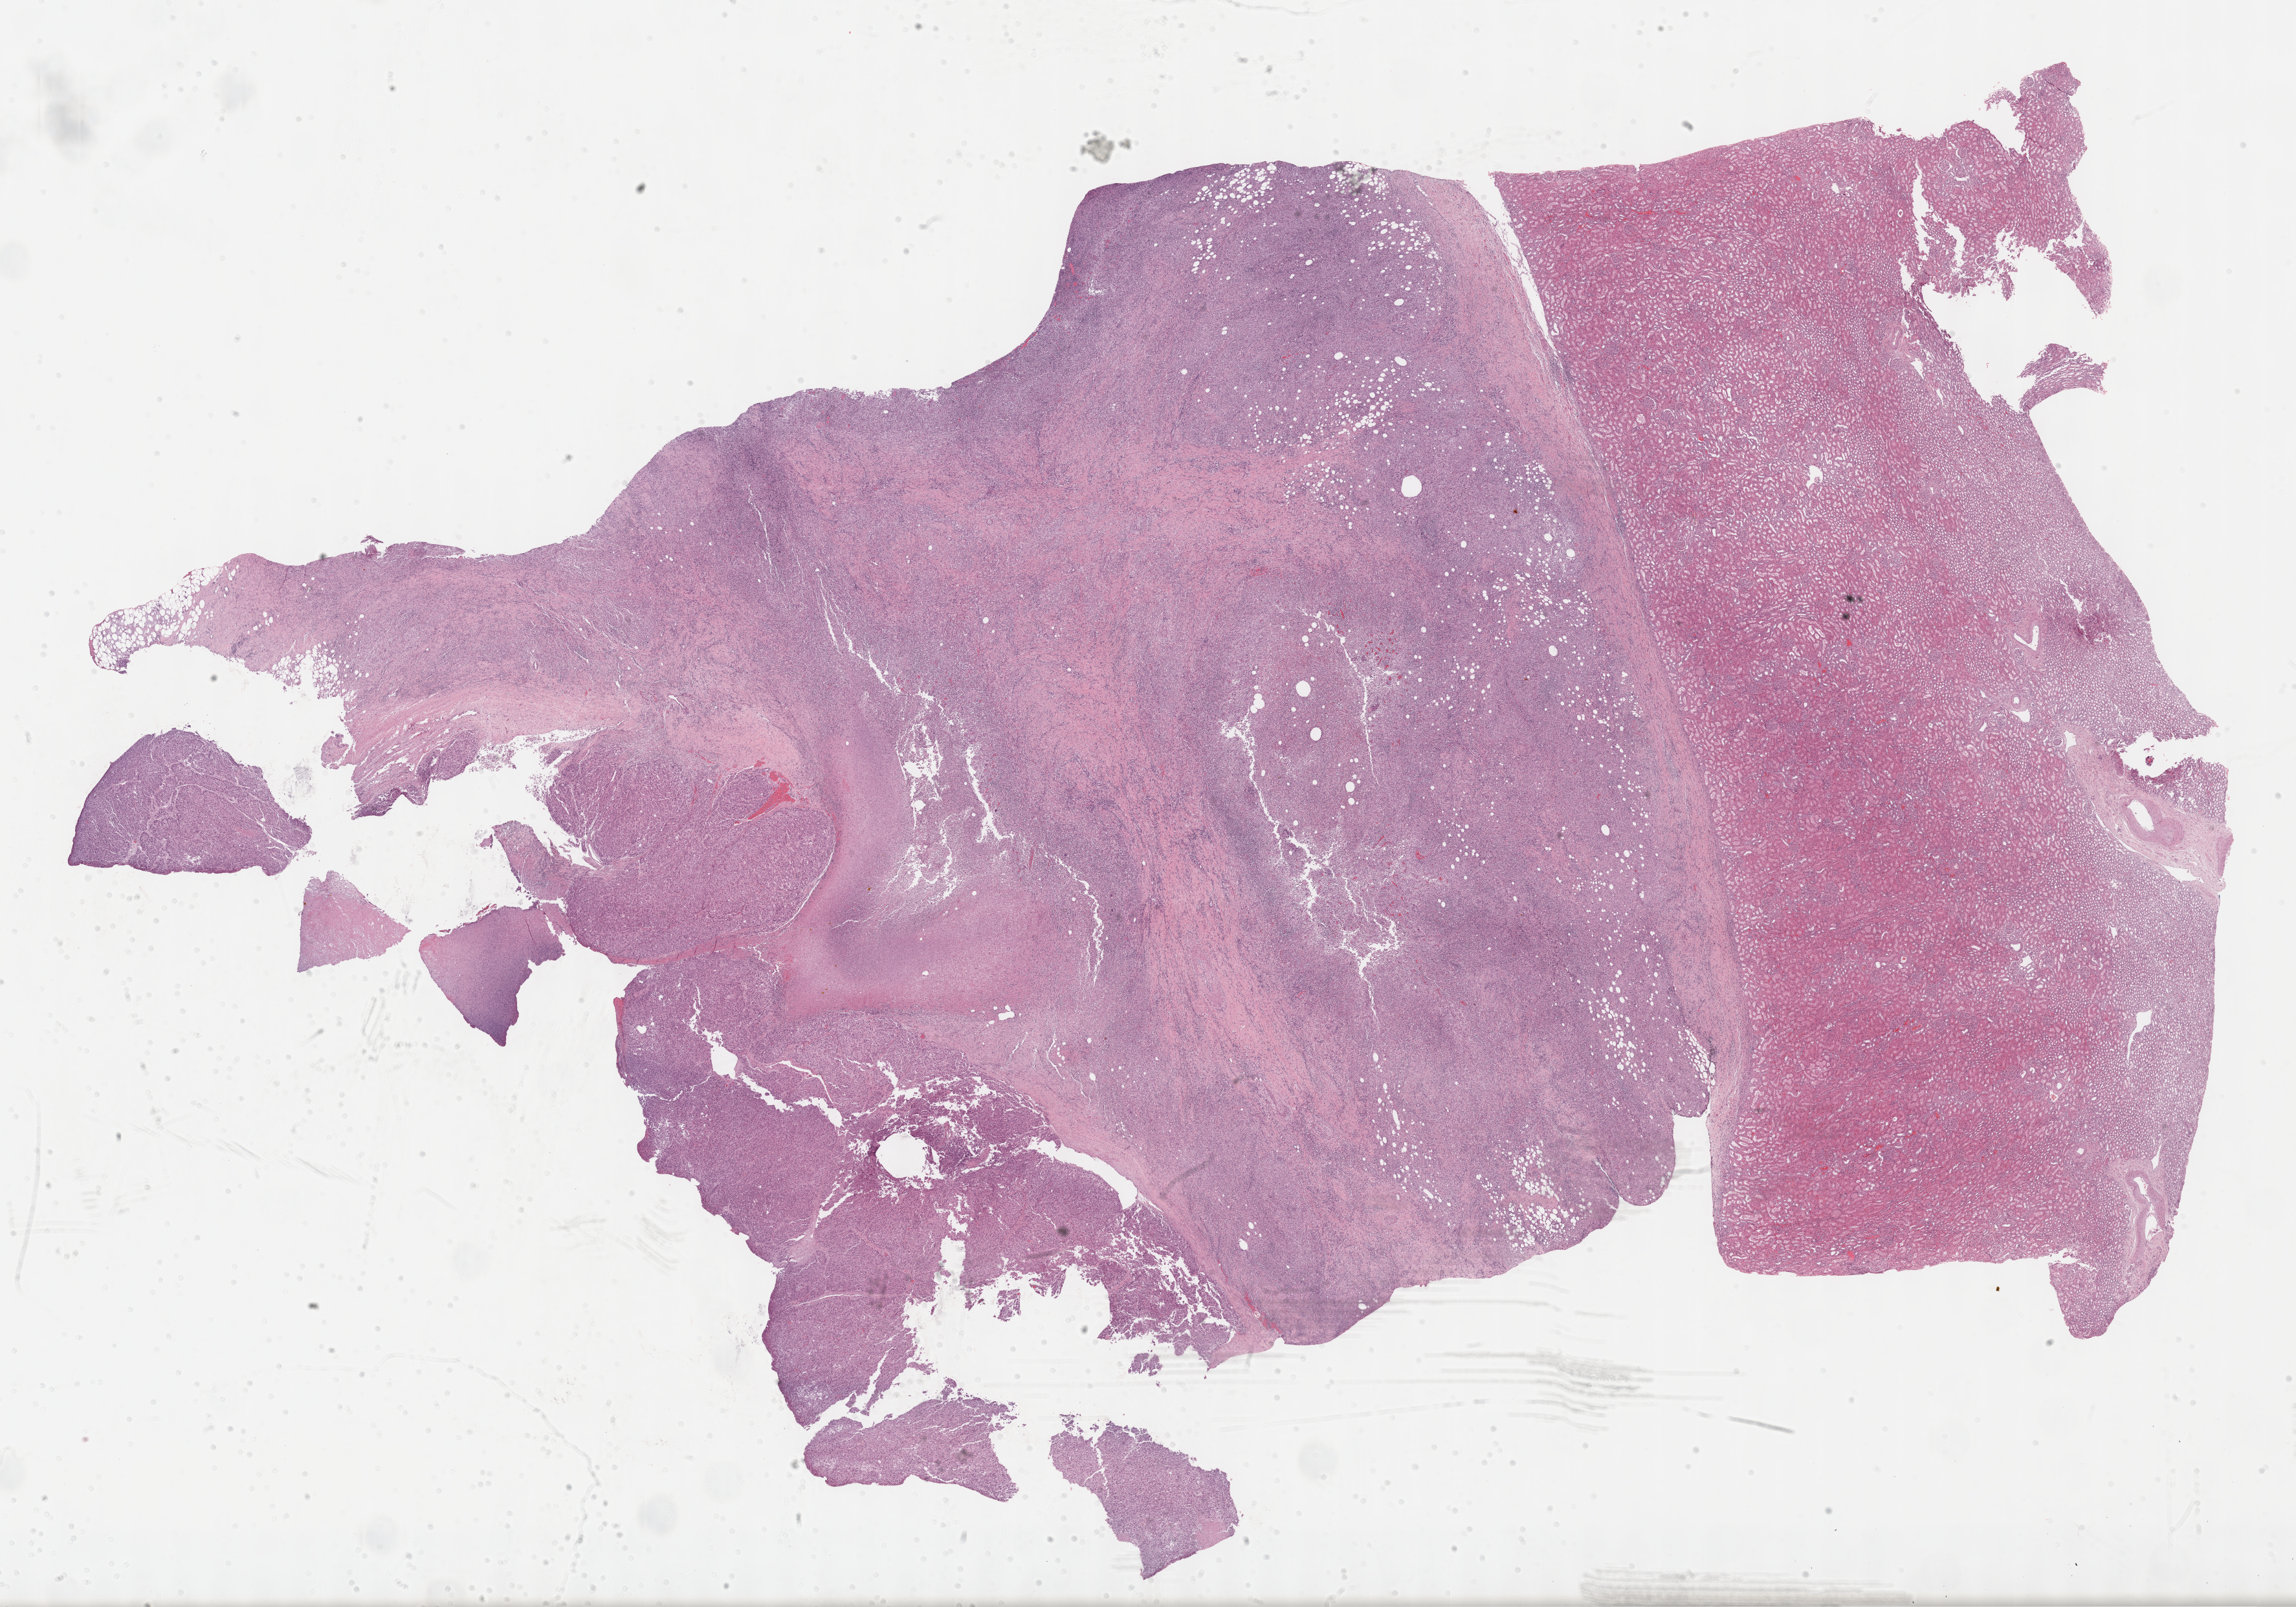
Digitized H&E-stained tissue section (whole slide) — shown as a low-resolution overview of the whole scanned area (about 28.7 x 20.1 mm); formalin-fixed paraffin-embedded (FFPE) diagnostic section; primary tumour sample from the adrenal cortex. Female patient; age at initial diagnosis 65 years.
Histologic diagnosis: Adrenal cortical carcinoma. Laterality: right.